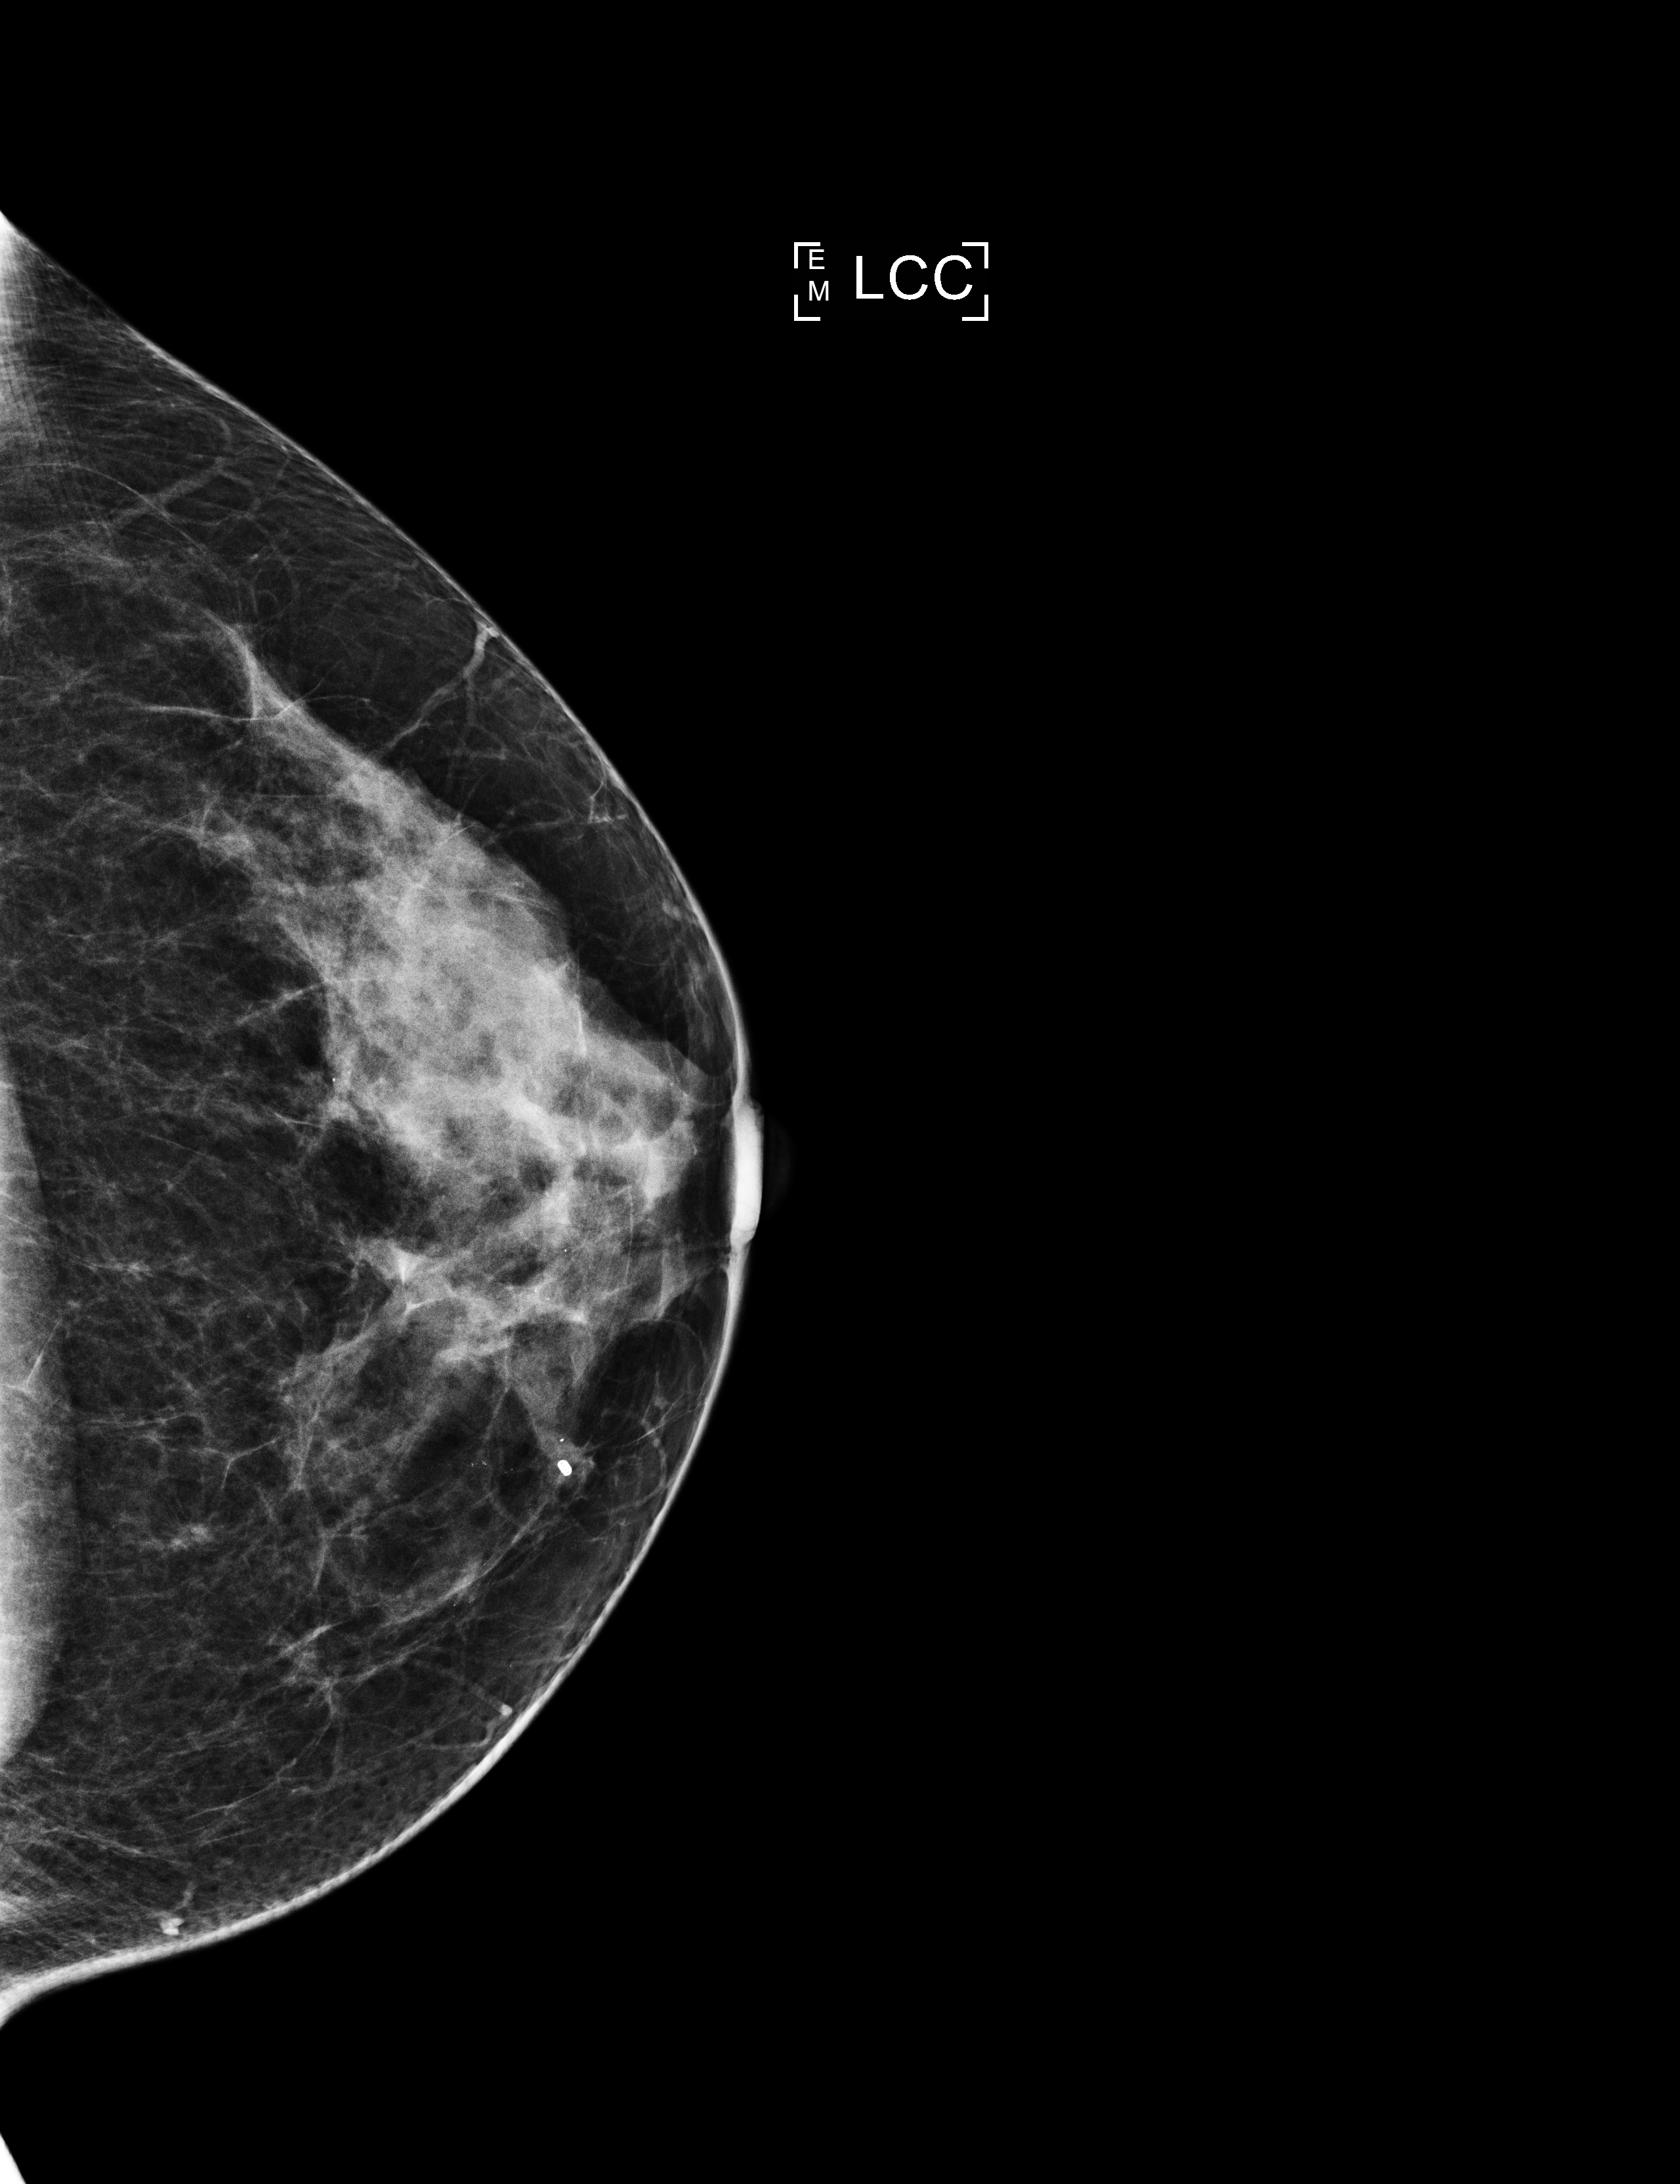
Full-field digital mammogram (FFDM); left breast; cranio-caudal projection; screening examination; system: Selenia Dimensions. Patient aged 56 years (female).
- breast density at the screening exam (both breasts): heterogeneously dense (BI-RADS density category c)
- final BI-RADS category for the screening round (tomosynthesis exam, both breasts): category 2
- recall: no recall after this screen